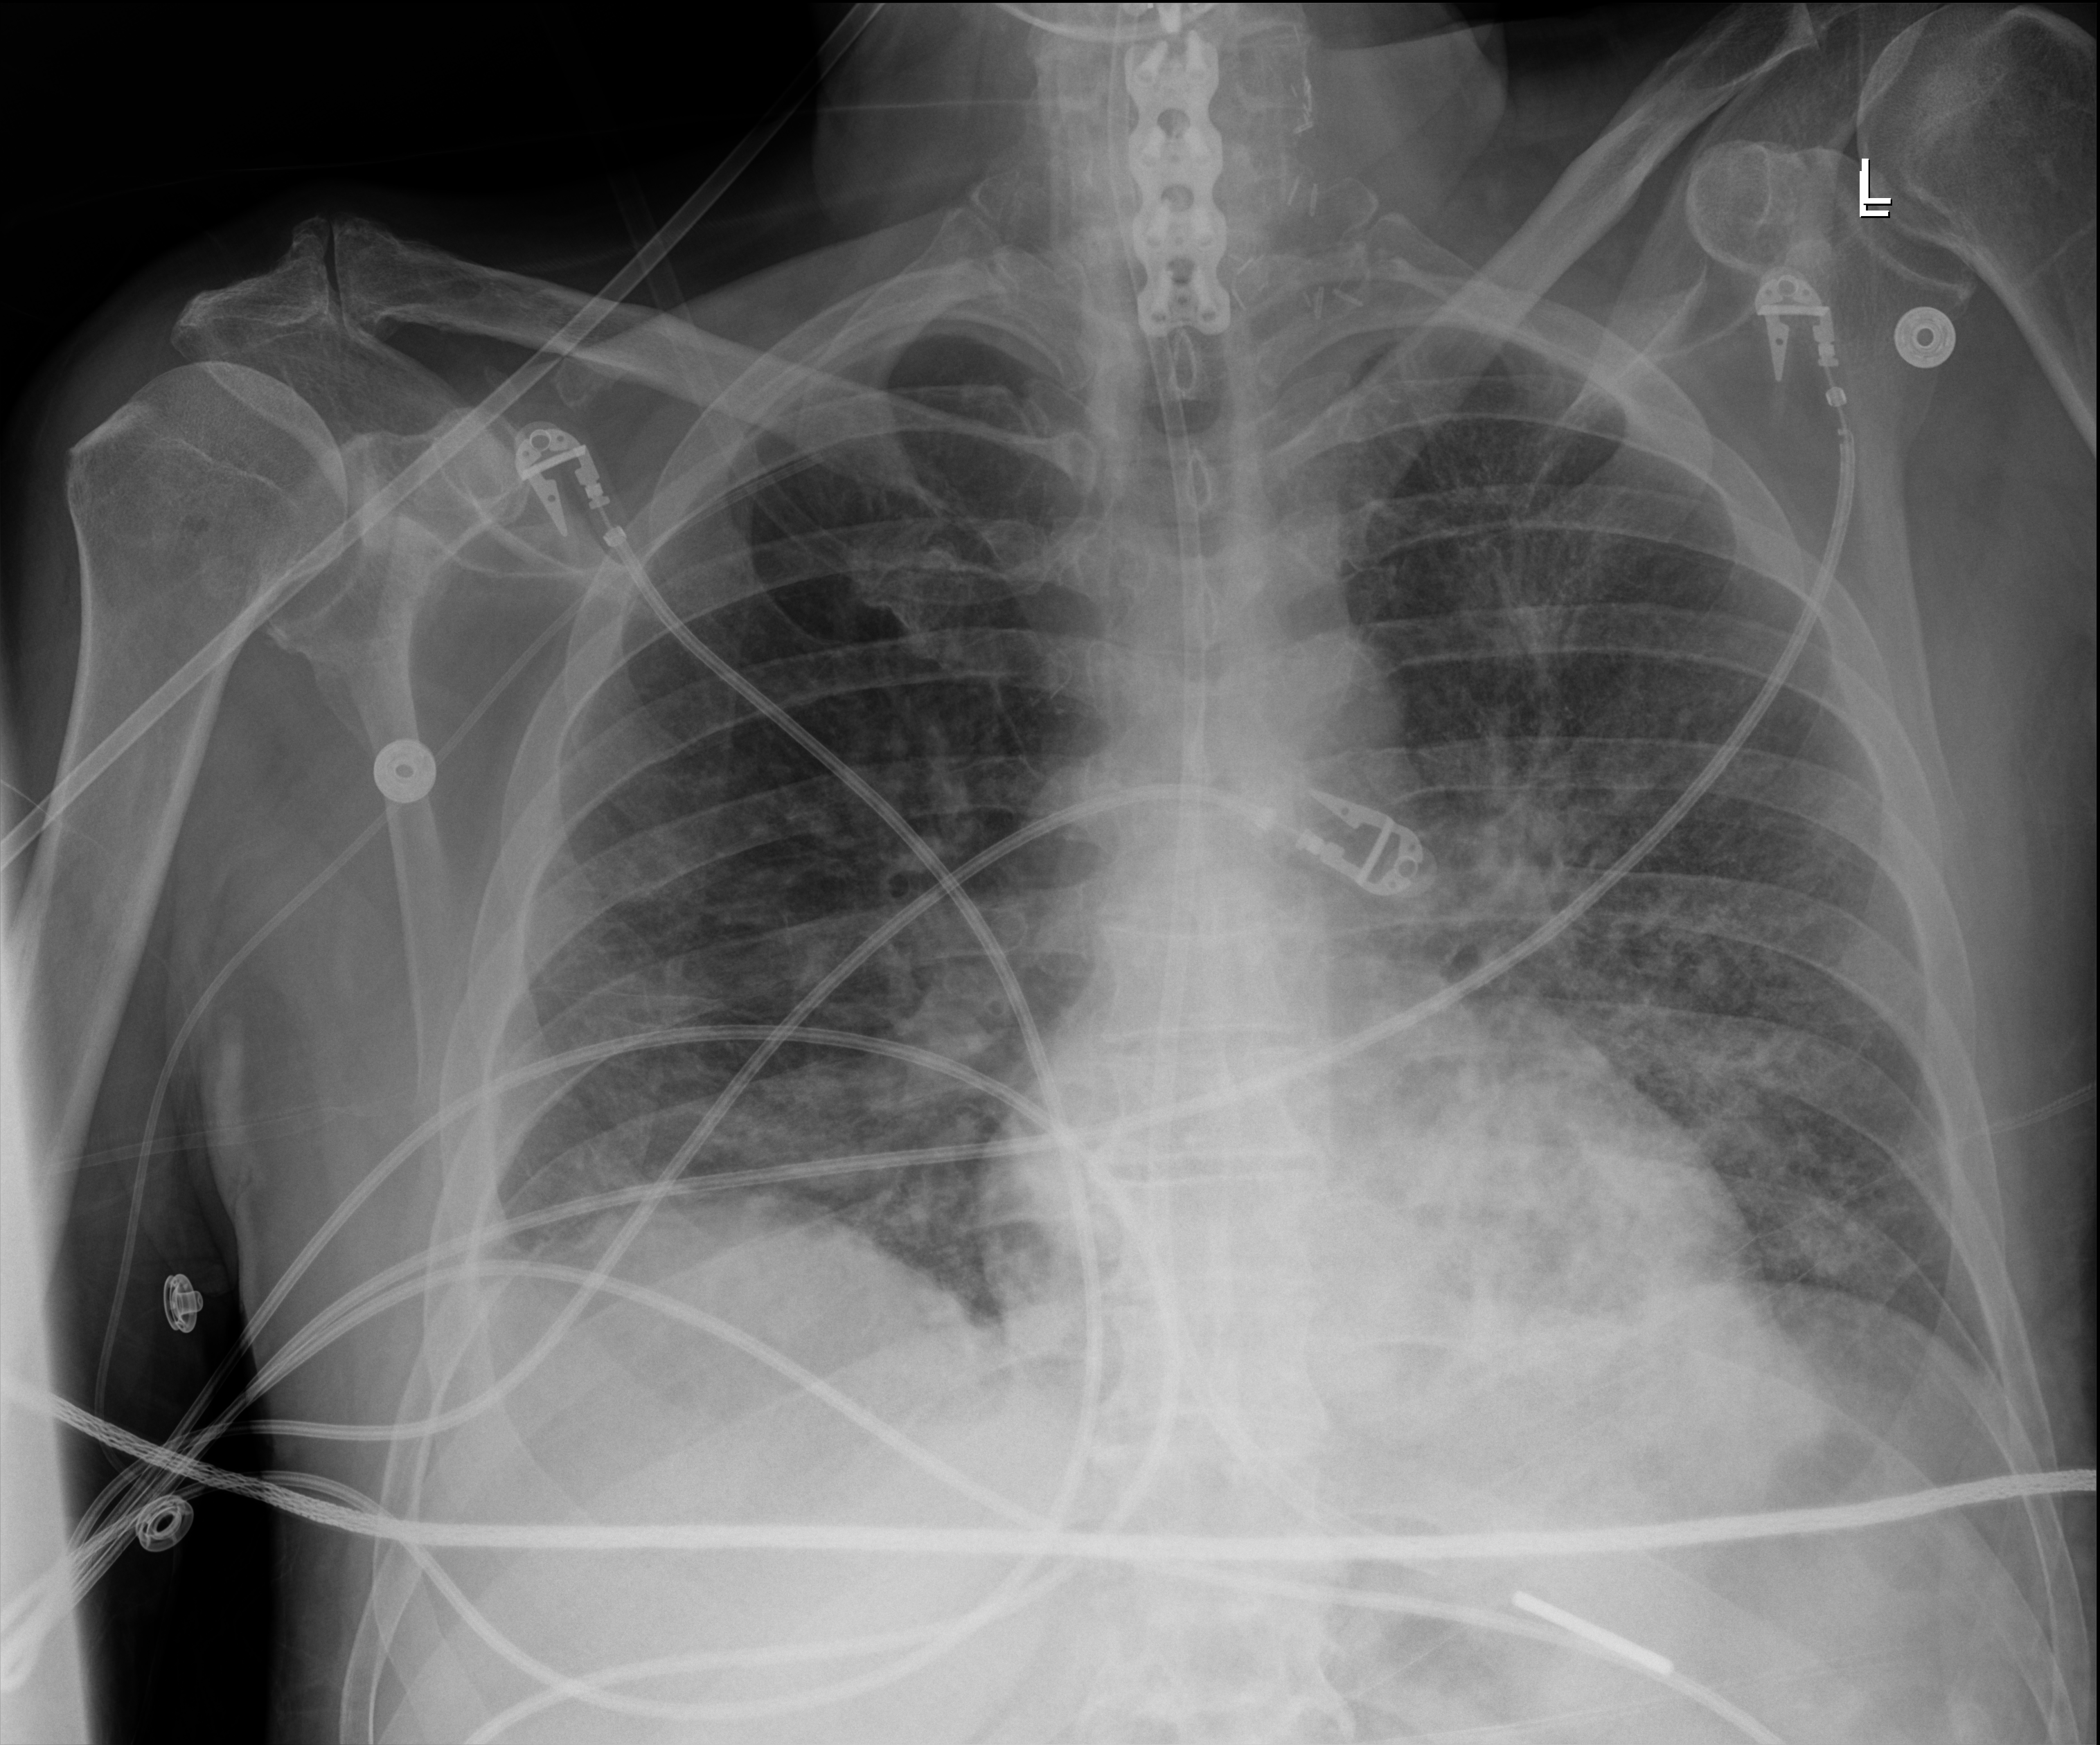
Portable chest radiograph; anteroposterior (AP) projection. Patient hospitalised with COVID-19; male, aged 60–74 years.
From the hospital-stay record, not from the radiograph (when in the stay this image was taken is not recorded): admitted to intensive care during this hospital stay: yes; mechanically ventilated during this hospital stay: yes.